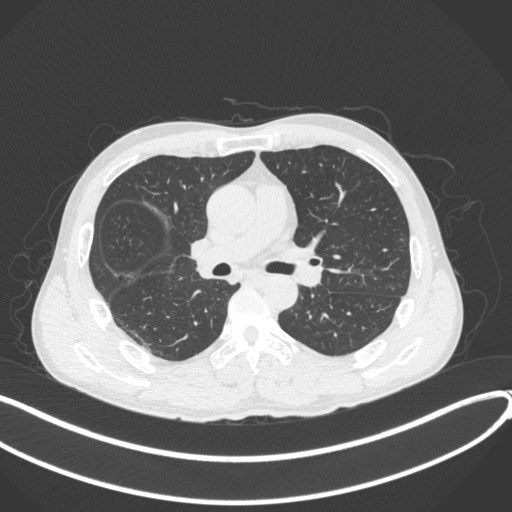
Chest CT, one axial slice; slice 224 of 409 in the series (ordered by position); reconstruction kernel B31f; lung window (W 1500 / L -600 HU); 1 mm slice thickness; 512 × 512 image matrix. Patient: male, 53 years. From the clinical record (not read from this slice): clinical TNM (as recorded): T1b N0 M0.
Structures marked on this image (rectangle marked by the reading radiologist):
- lung tumour (recorded histology: squamous cell carcinoma): bounding box <185,232,228,283> (left, top, right, bottom; pixels)